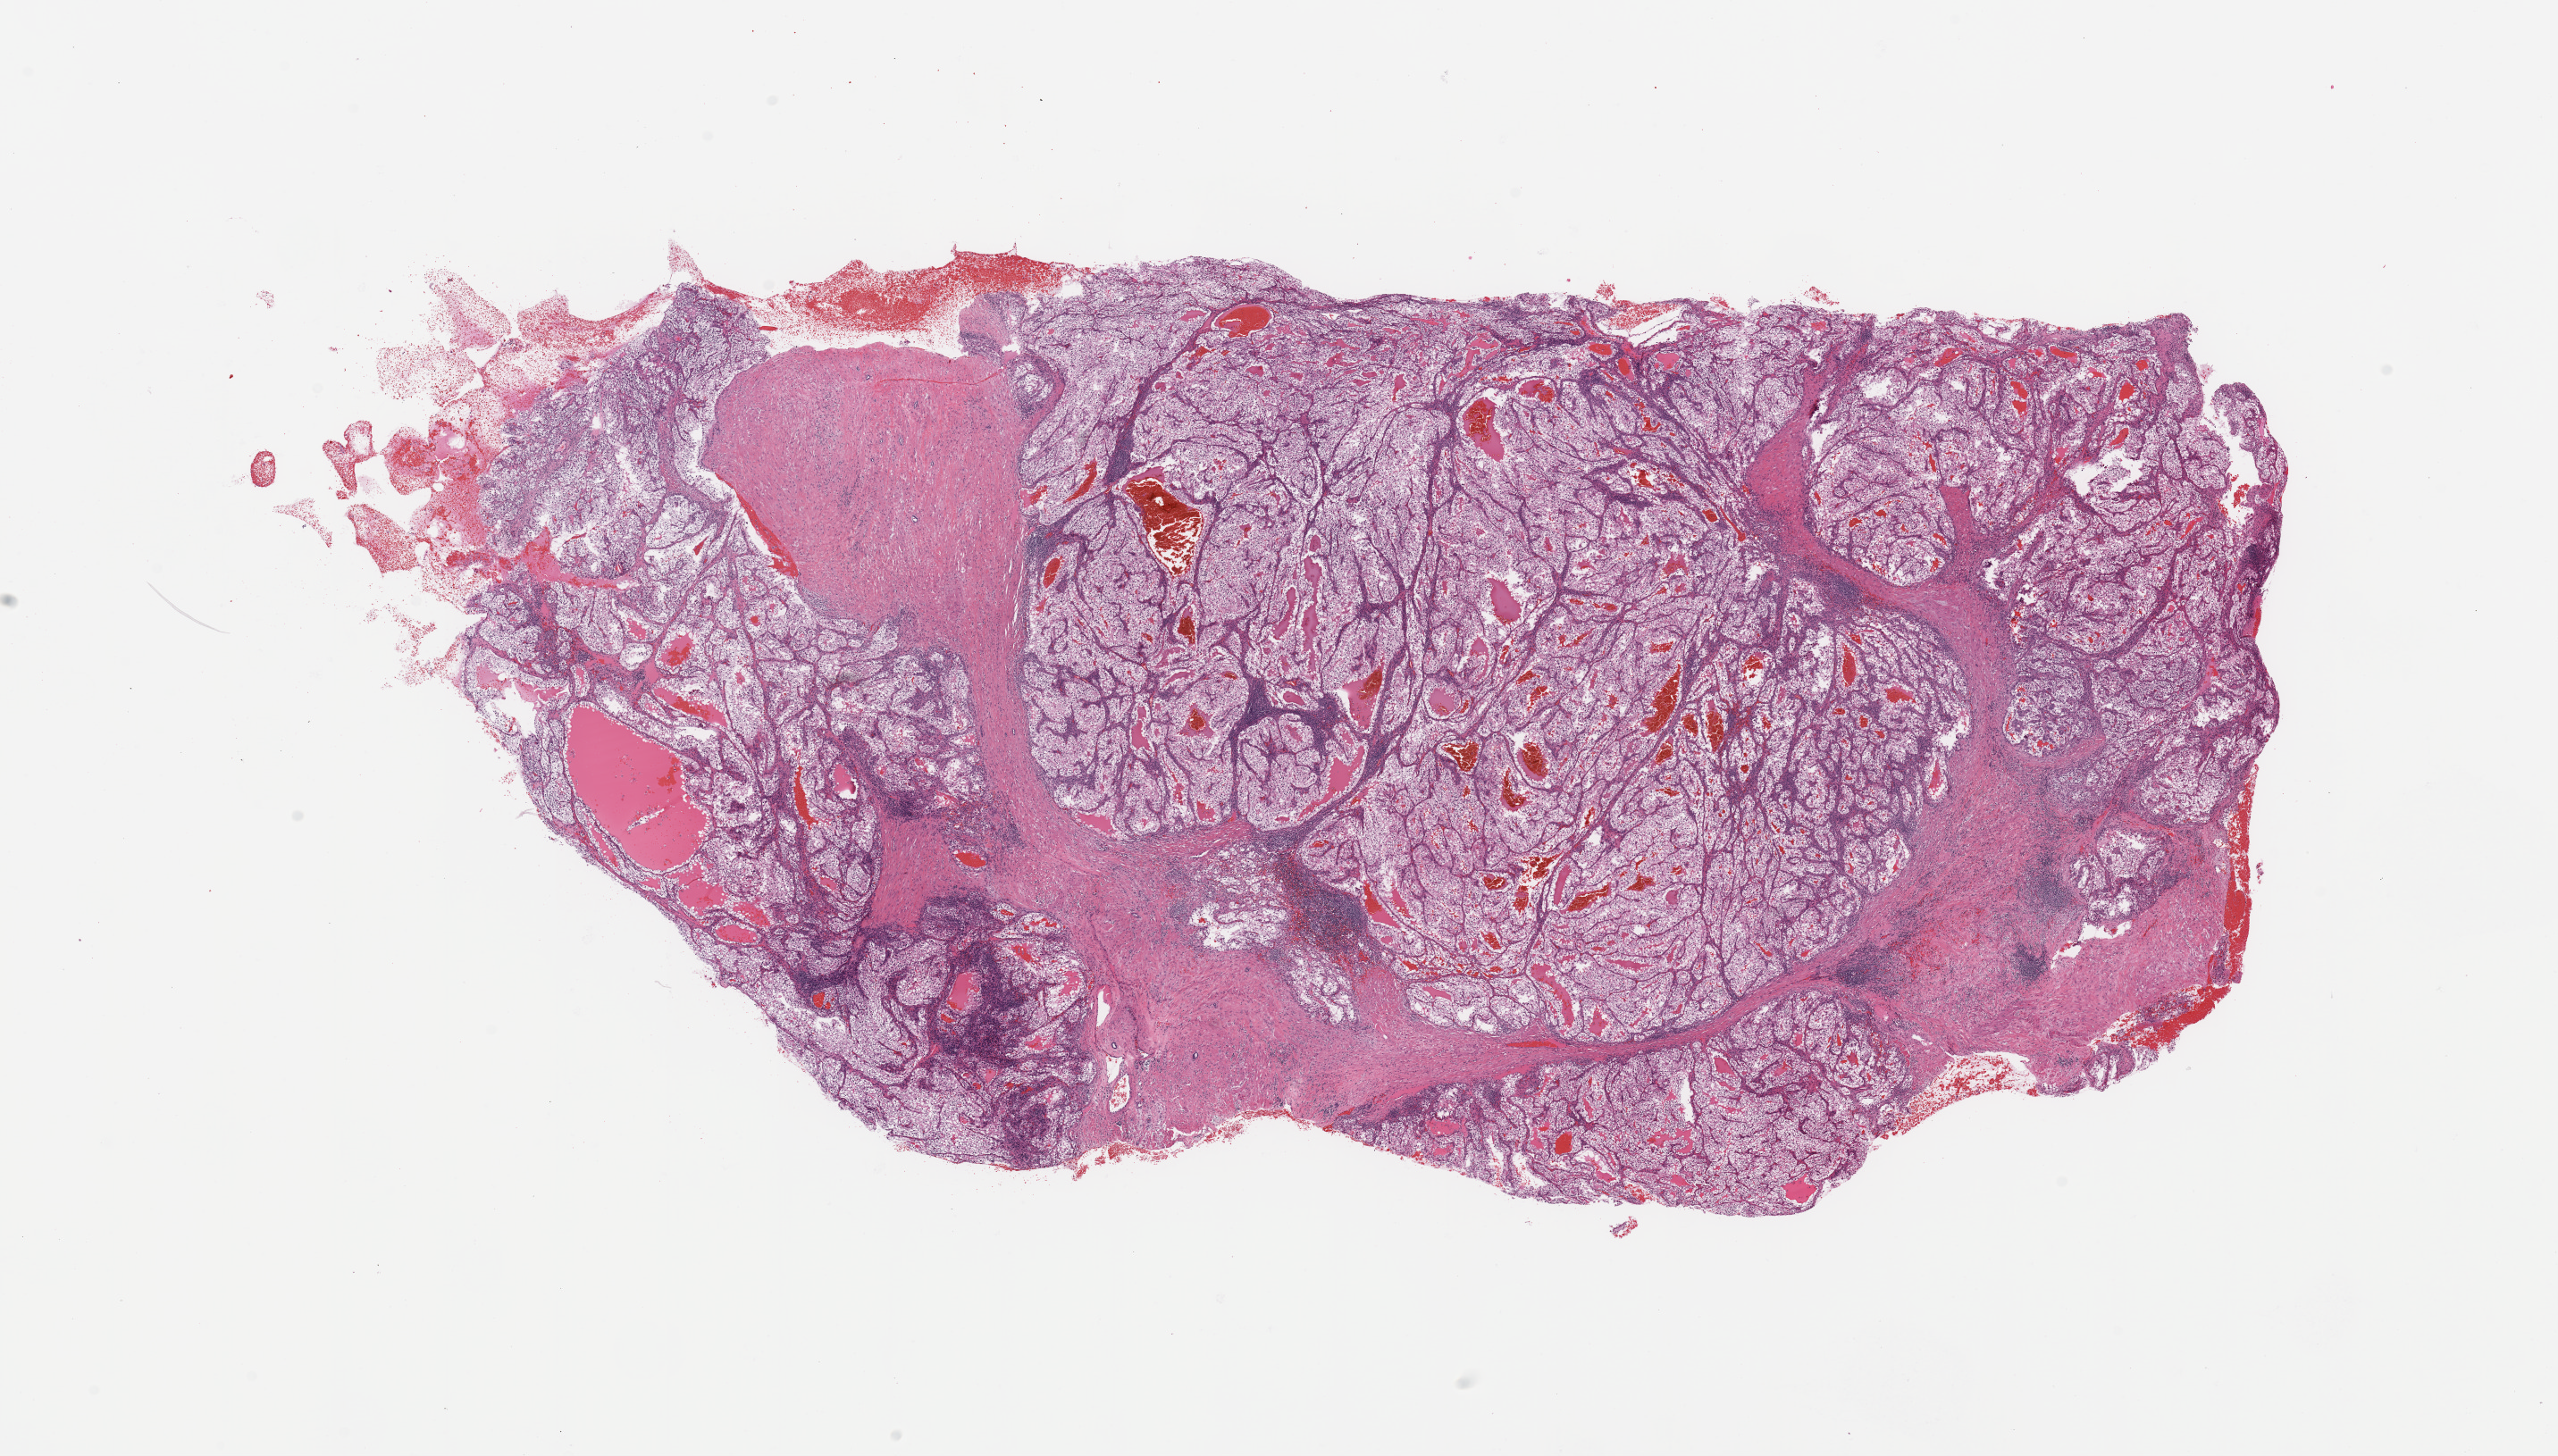
Digitized H&E-stained tissue section (whole slide) — a low-resolution overview of the entire scanned area, about 22.6 x 12.9 mm (slide scanned at 20x); tumour tissue sample, kidney. Male, 55 y/o. Histologic grade: G3 (poorly differentiated).
Histologic diagnosis: Renal cell carcinoma, NOS. AJCC pathologic stage: IV.